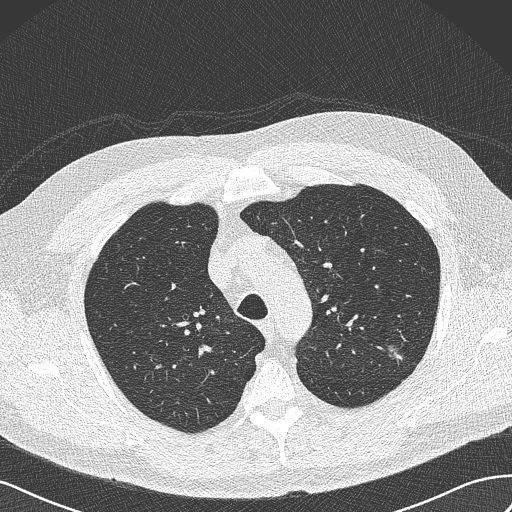
Axial slice from a low-dose chest CT screening exam. Baseline screening round. Lung window (W 1500 / L -600 HU). Lung (sharp) reconstruction kernel (B50f). Slice 105 of 462 in the series. 512 × 512 image matrix, field of view 360 × 360 mm. Male participant, aged 65 years at enrolment. Former smoker at enrolment.
• Lesion marked by an expert reader, box from (x=383, y=341) to (x=417, y=373) px.
• The screening reader recorded 3 non-calcified nodules or masses ≥4 mm on this exam (left upper lobe, left upper lobe, right upper lobe); which of them this box marks is not recorded.
• Later outcome: lung cancer diagnosed 541 days after this screen — adenocarcinoma, NOS, left upper lobe, poorly differentiated (G3), stage IA (AJCC 6th edition), 13 mm at pathology.